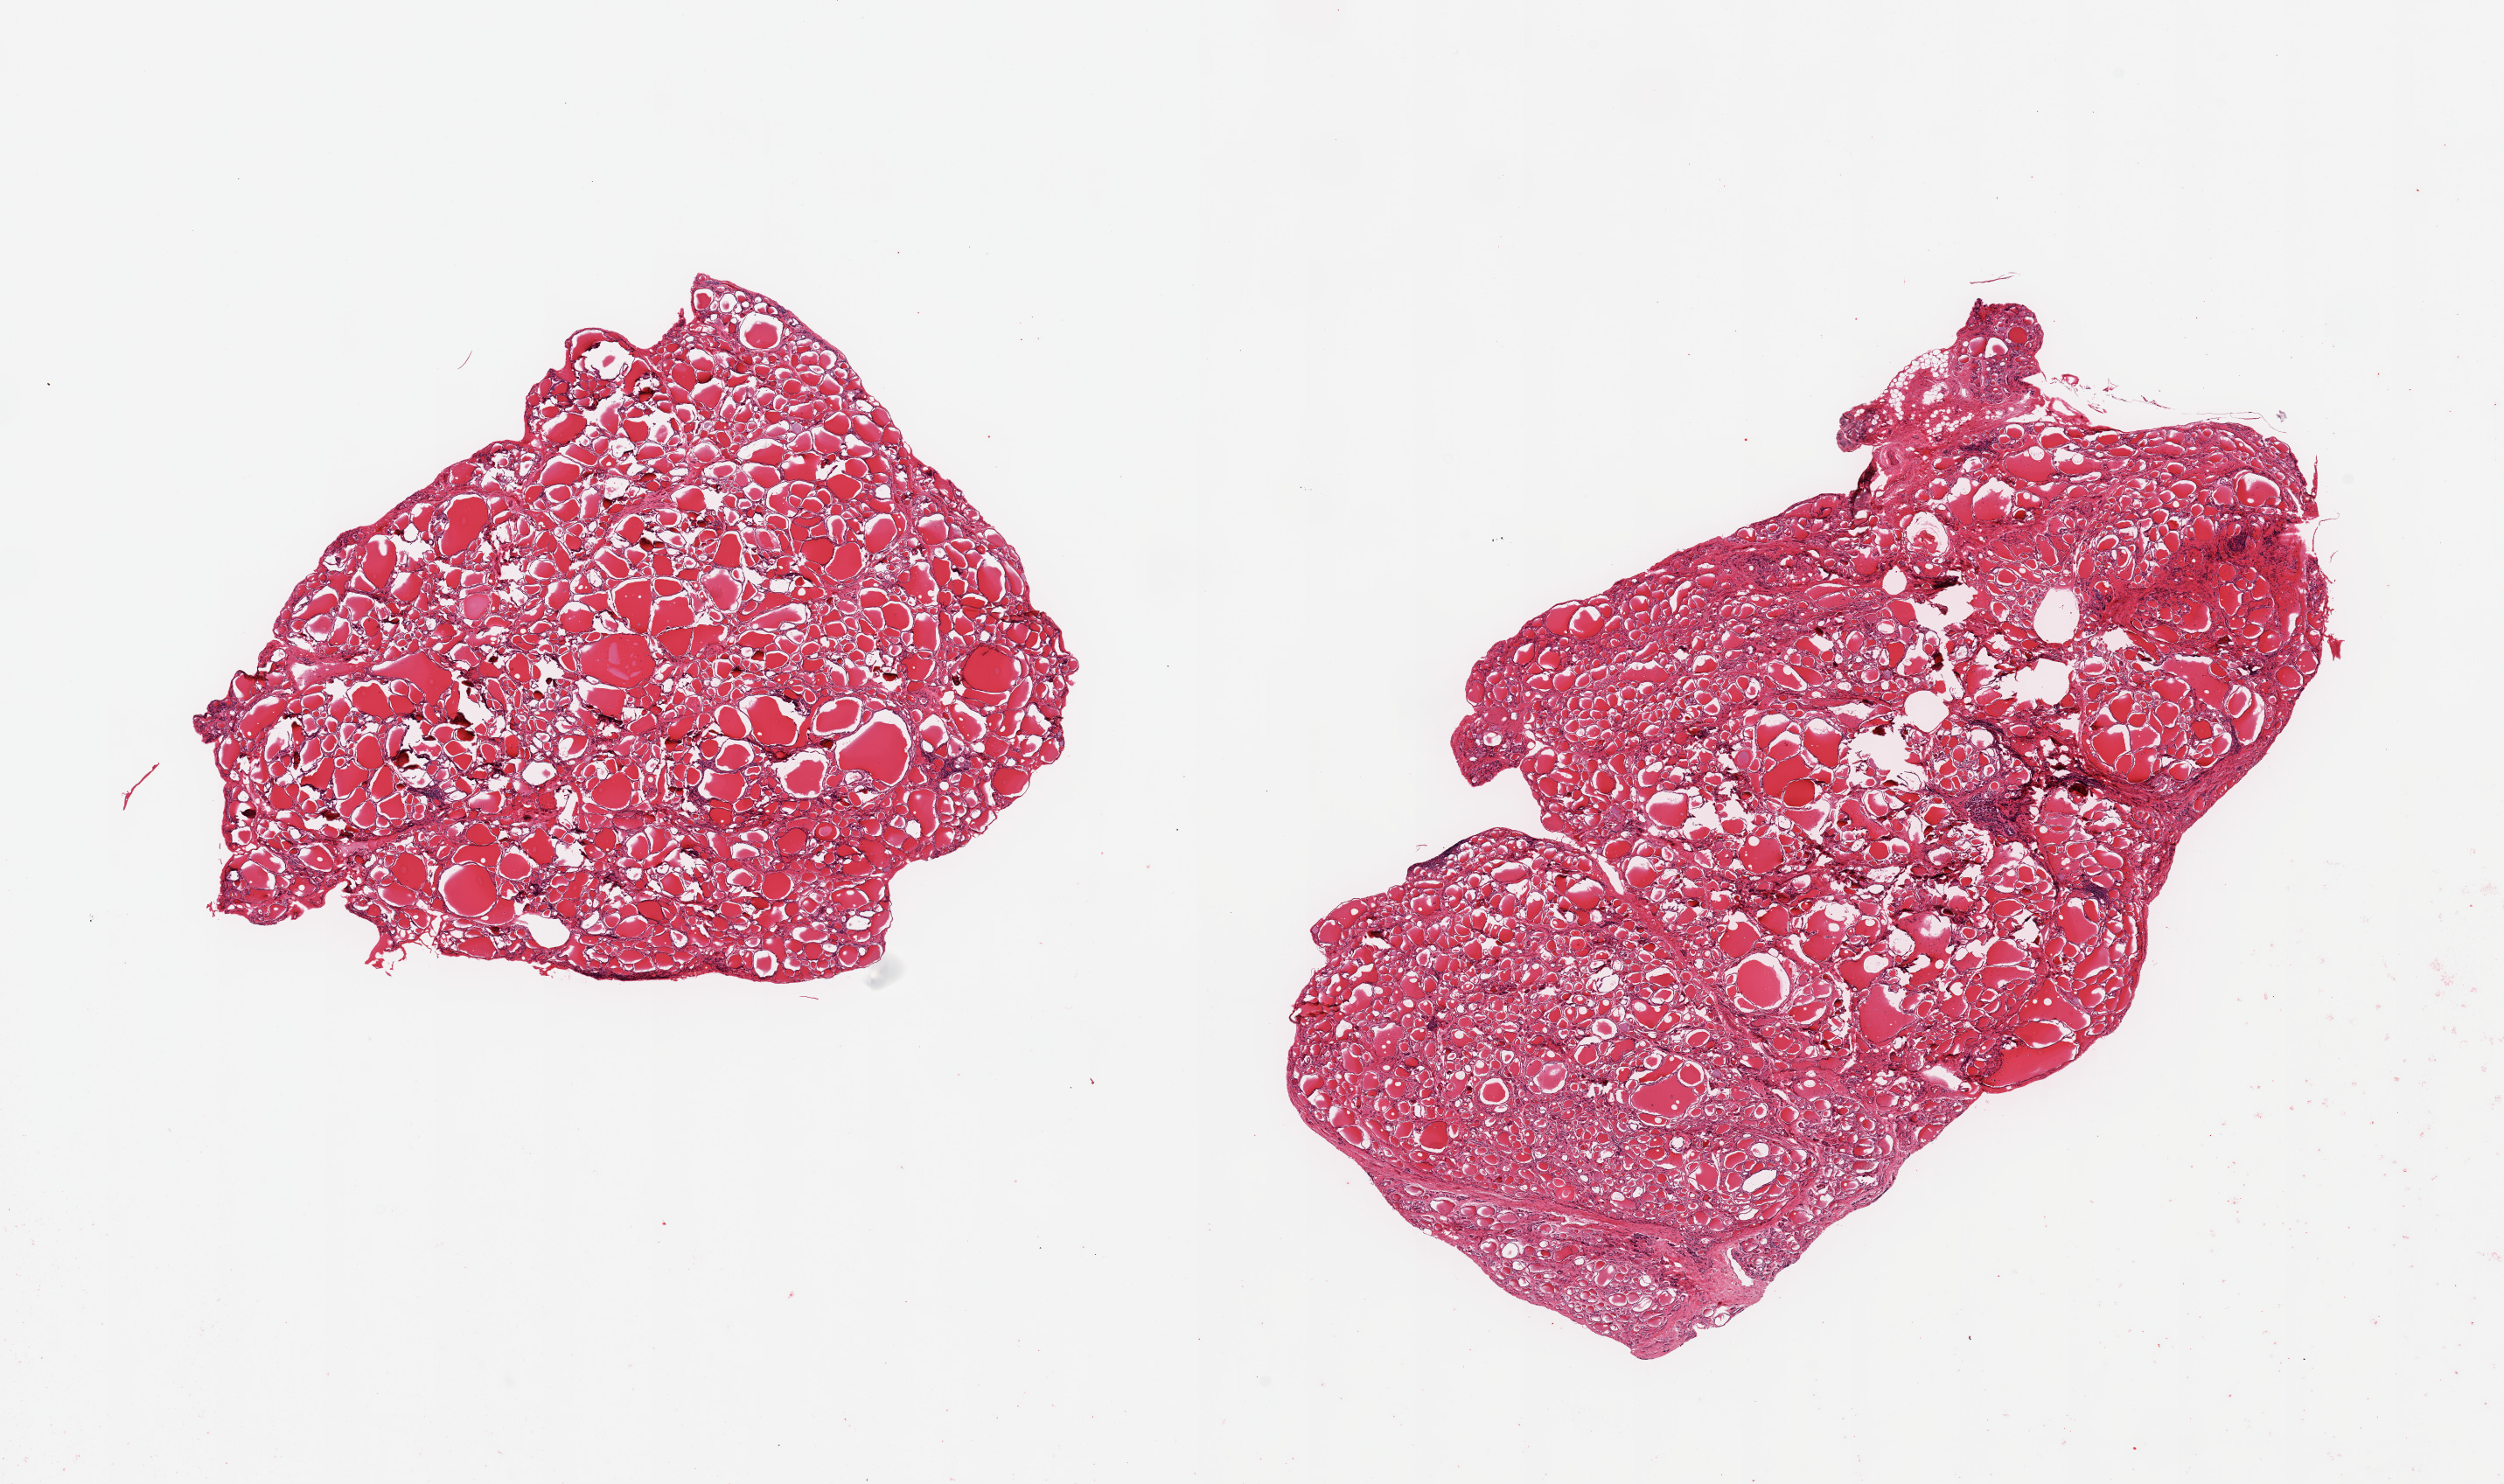
H&E whole-slide image, low-resolution overview of the scanned area, about 22.6 x 13.4 mm; PAXgene-fixed, paraffin-embedded tissue; target tissue: thyroid; tissue donor sample.
Pathologist's review note for this sample: 2 pieces, no abnormalities.